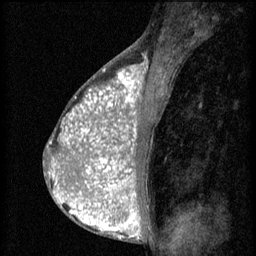
Breast MRI (dynamic contrast-enhanced), one sagittal slice; slice 33 of 60 in the series (ordered by position); 3 images stored at this slice position (order not interpretable as contrast timing); 1.5 T; TE 4.2 ms, TR 8.2 ms; 2 mm slice thickness; 256 × 256 image matrix. Female patient, age 38 years.
Outlined on this slice (semi-automatic segmentation, software-assisted and operator-edited):
- analysis volume of interest (the breast-tissue region the enhancement analysis was run in; not a lesion): bounding box [x1, y1, x2, y2] px = [92, 112, 152, 171]
- tumour enhancement mask (voxels above the 70 % enhancement threshold inside the analysis volume of interest): [93, 112, 137, 171]